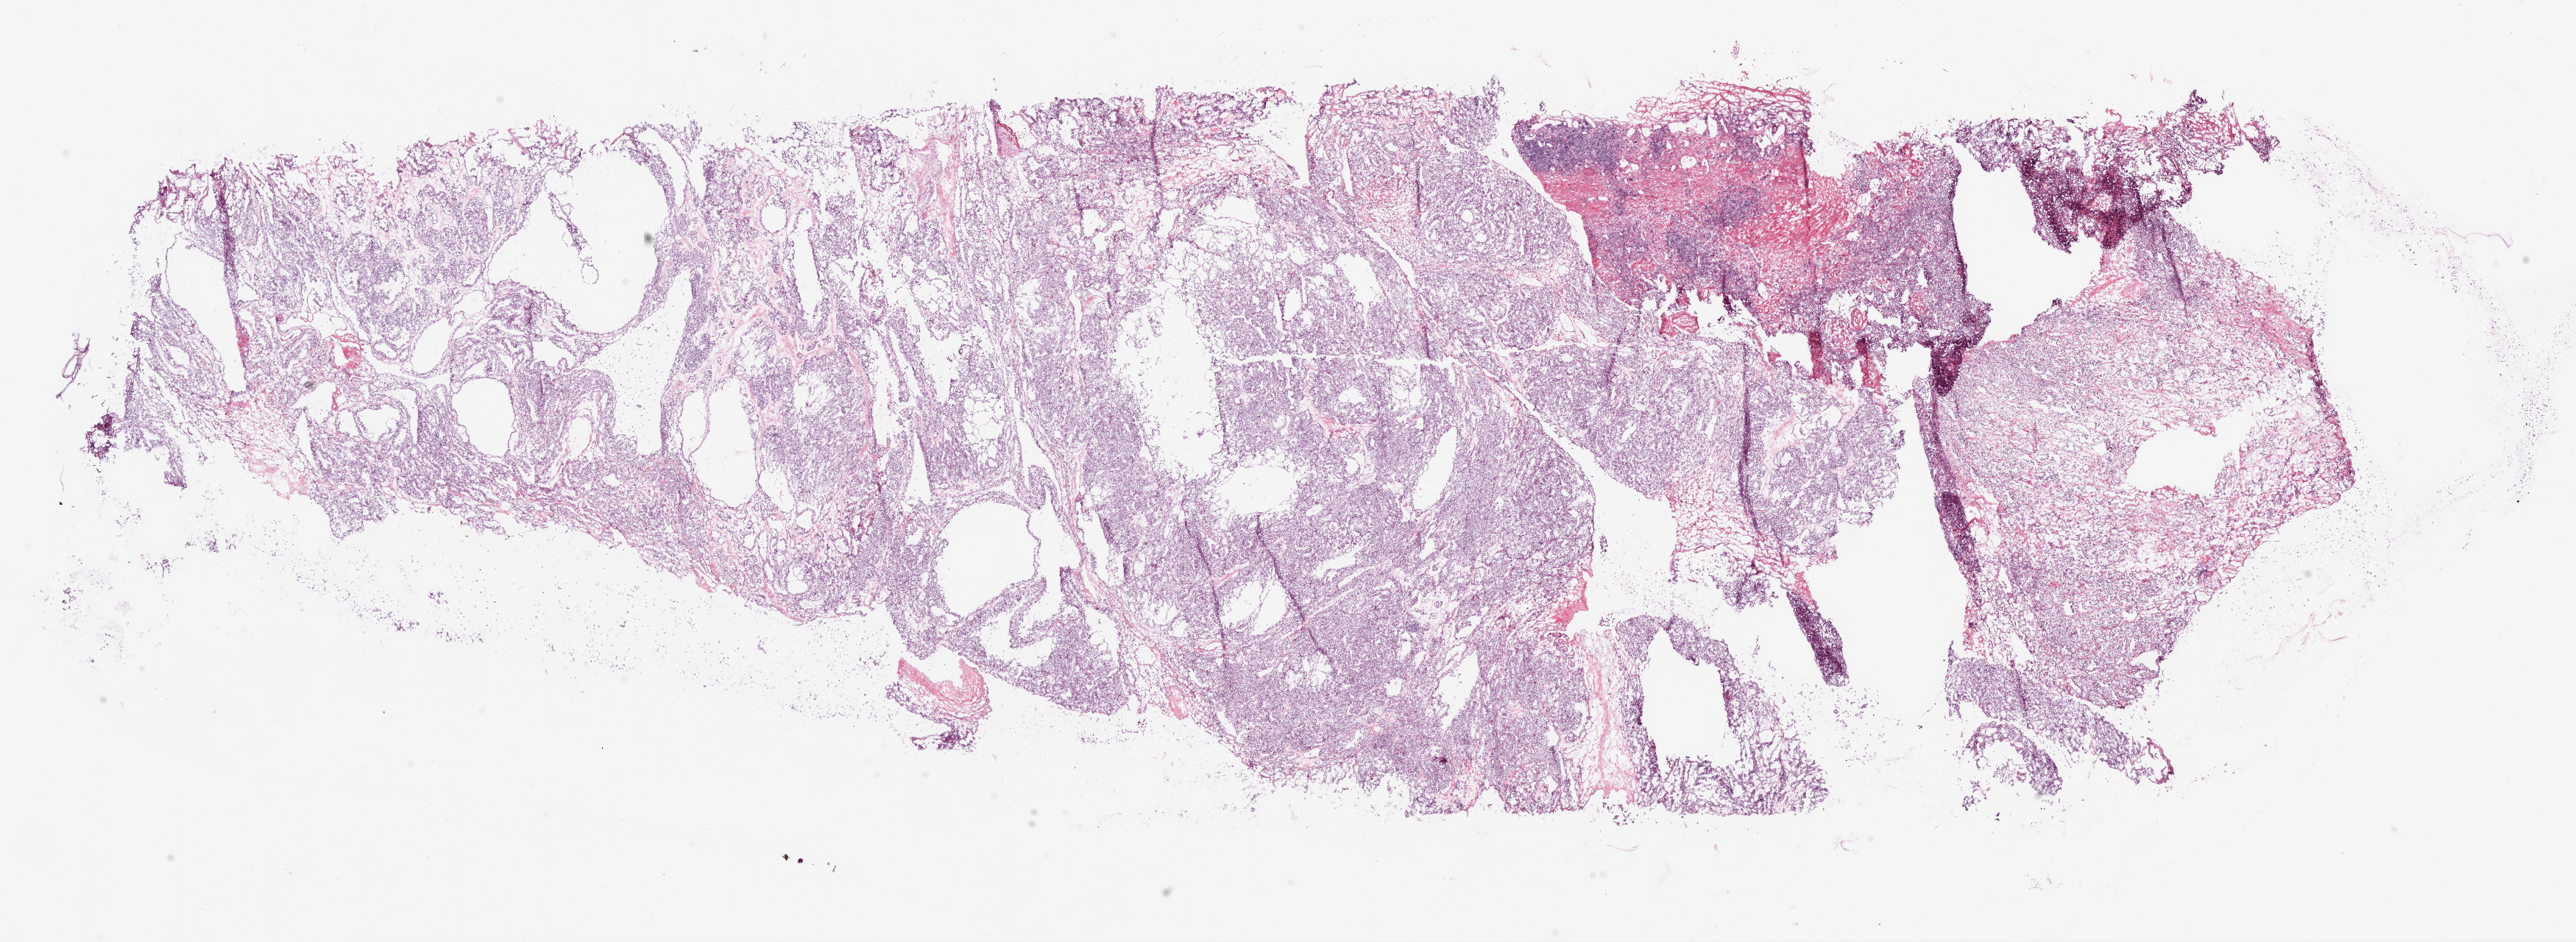
Digitized H&E-stained tissue section (whole slide), low-resolution overview of the scanned area, about 28.1 x 10.3 mm (acquisition: 20x scan). Frozen section from the bottom of the tissue portion. Primary tumour sample from the kidney. Male, age 50 years at initial diagnosis. Histologic grade: G3 (poorly differentiated). Pathologist review of this section (percent, as recorded): tumour cells 85%, tumour nuclei 75%, normal cells 0%, stromal cells 15%, necrosis 0%.
* AJCC pathologic stage: I
* pathologic diagnosis: Clear cell adenocarcinoma, NOS